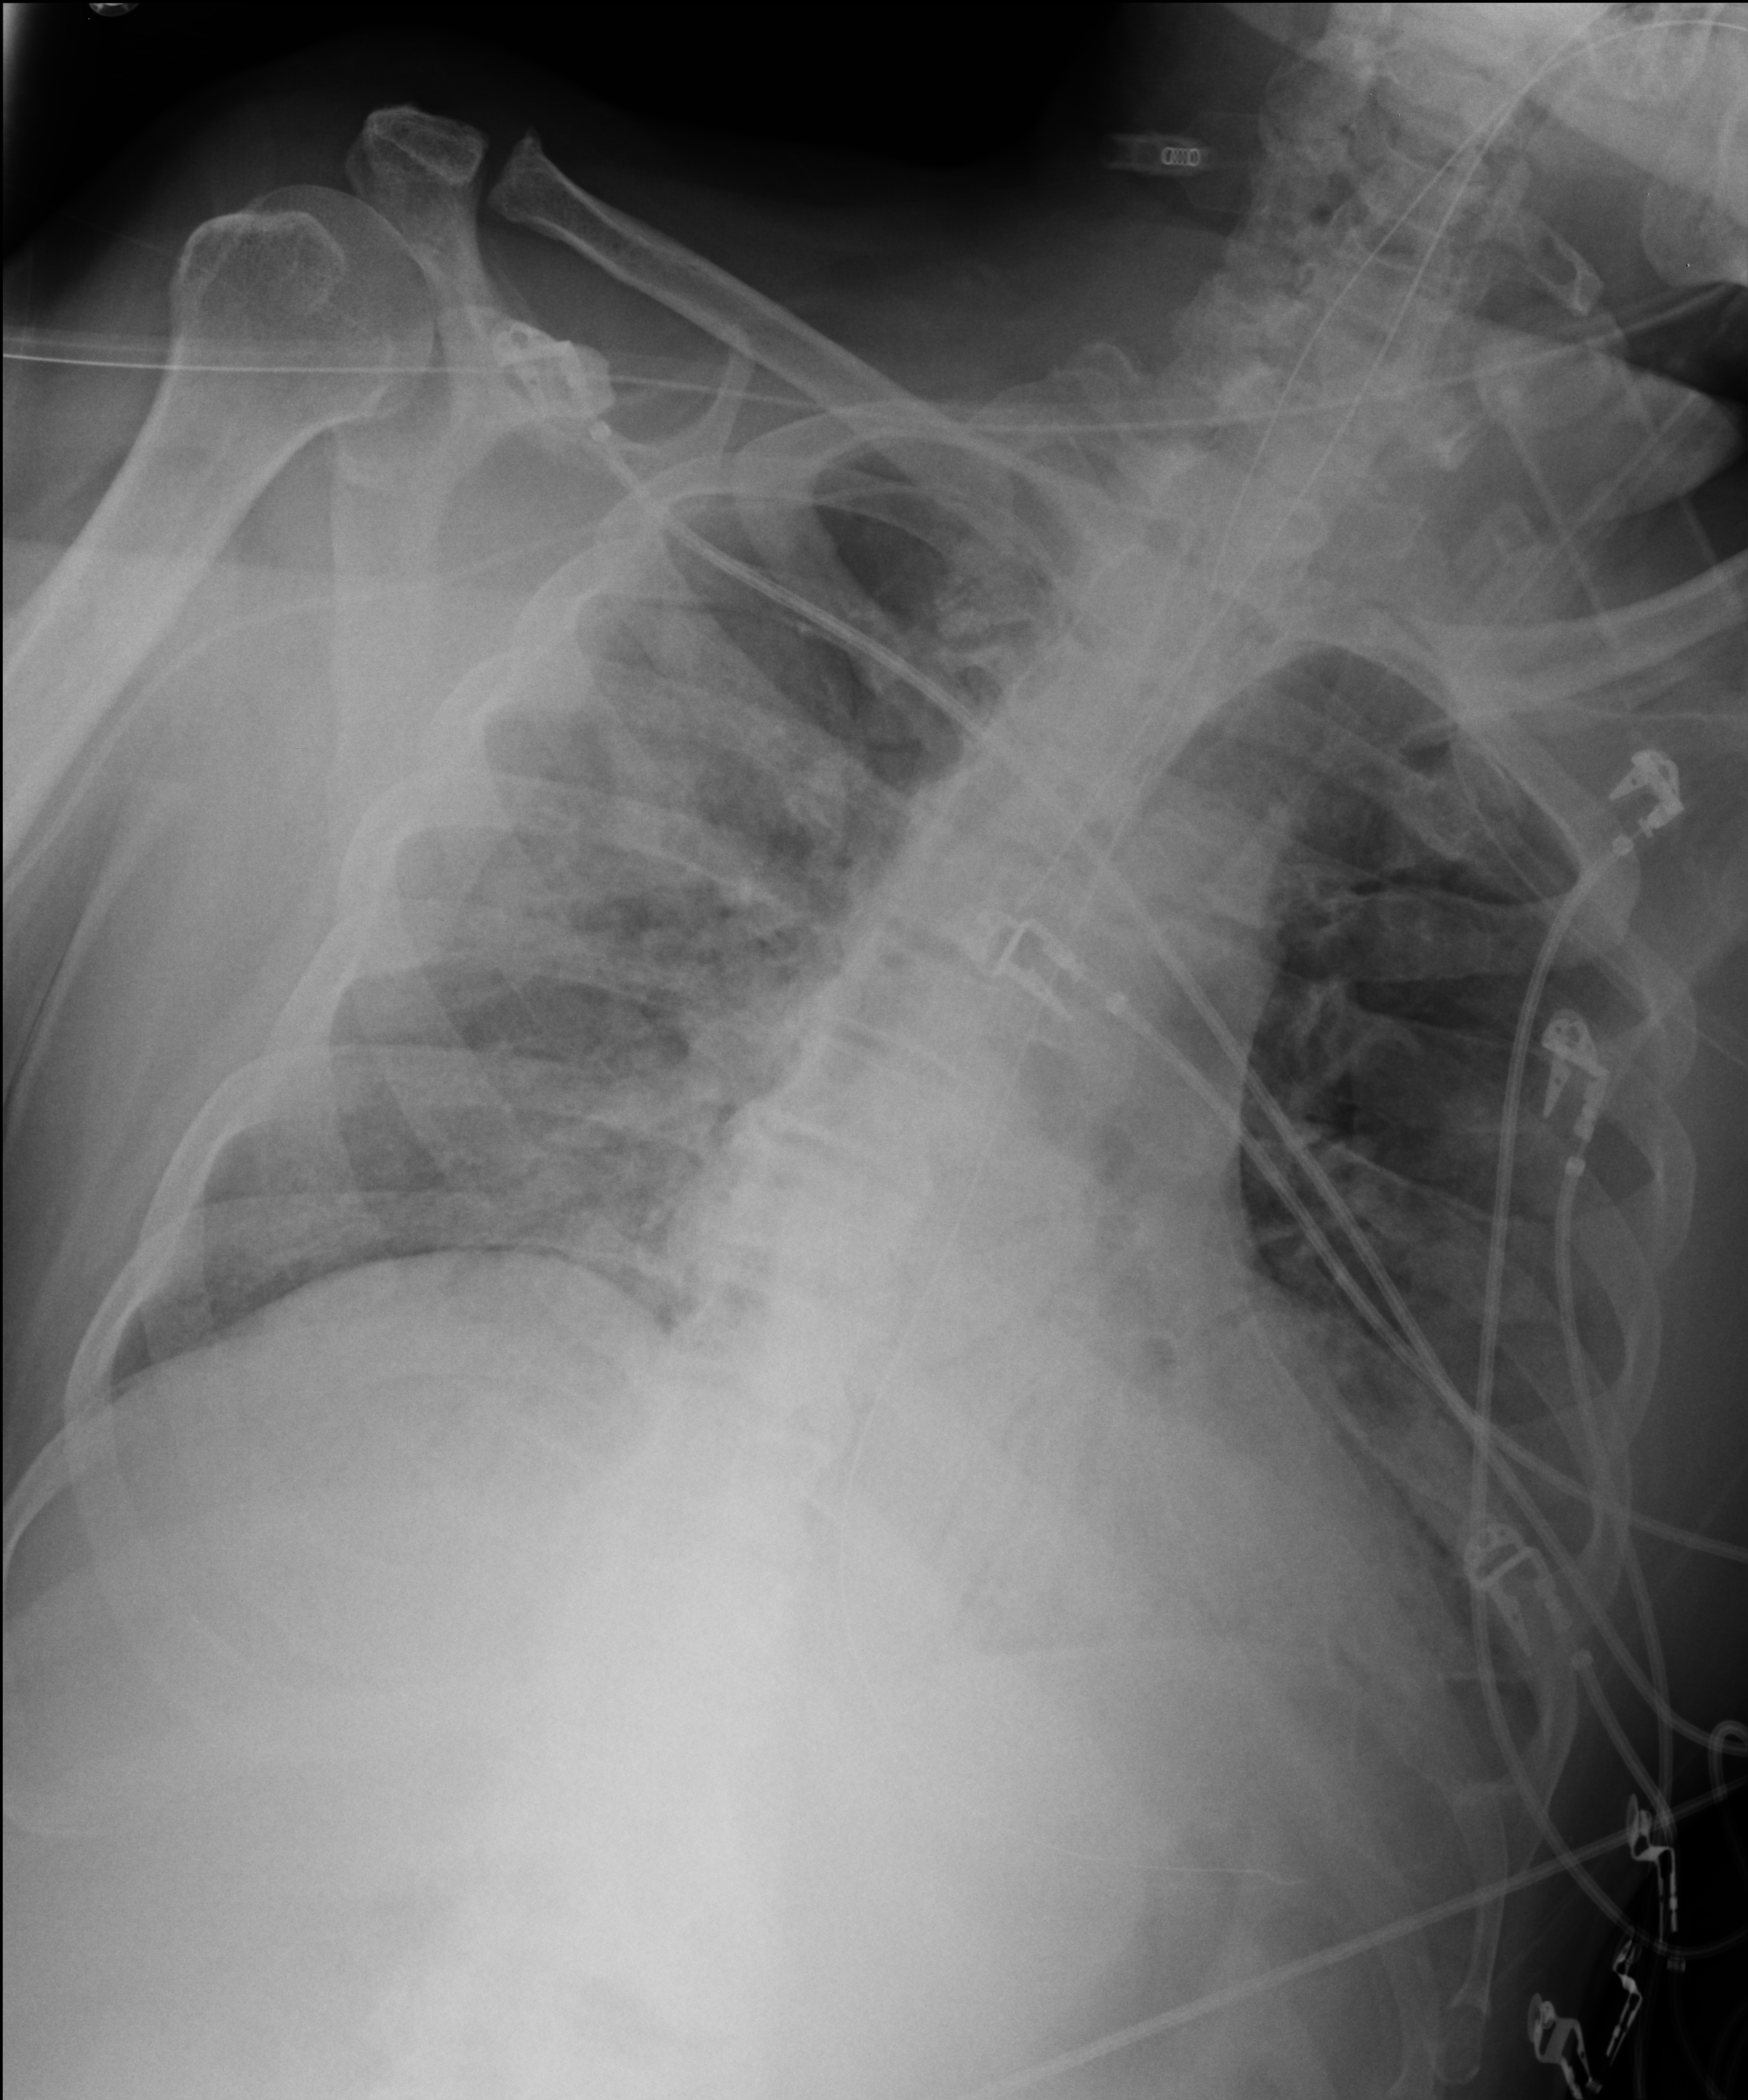
Portable chest radiograph; anteroposterior (AP) projection. Patient hospitalised with COVID-19; male, aged 75–90 years.
Admission-level facts for this patient (not findings on this image; timing relative to this image not recorded):
- mechanically ventilated during this hospital stay: yes